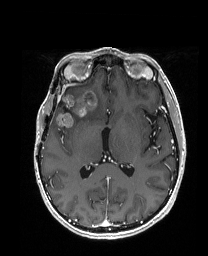
Brain MRI from a brain-tumour surgery series, one axial slice; T1-weighted post-contrast; 1 mm slice thickness; 208 × 256 image matrix, field of view 203 × 250 mm. From the clinical record (not read from this slice): histopathology: Metastatic Carcinoma from Breast primary; tumour location: Right Frontal.
Outlined on this slice (manually delineated by an expert):
- previous resection cavity: bounding box <58,101,68,111> (left, top, right, bottom; pixels)
- tumour: <62,89,104,126>